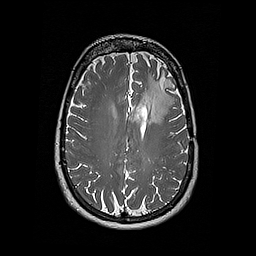
Brain MRI from a brain-tumour surgery series, one axial slice; position 121 of 192 along the scan axis; 1 mm slice thickness; 256 × 256 image matrix, field of view 250 × 250 mm. Case-level facts recorded for this patient, not image findings: histopathology: Oligodendroglioma; WHO grade: 2; IDH mutation: yes; tumour location: Left Frontal.
Annotated regions visible in this slice (outlined manually by an expert reader):
- tumour: bounding box <139,74,174,124> (left, top, right, bottom; pixels)